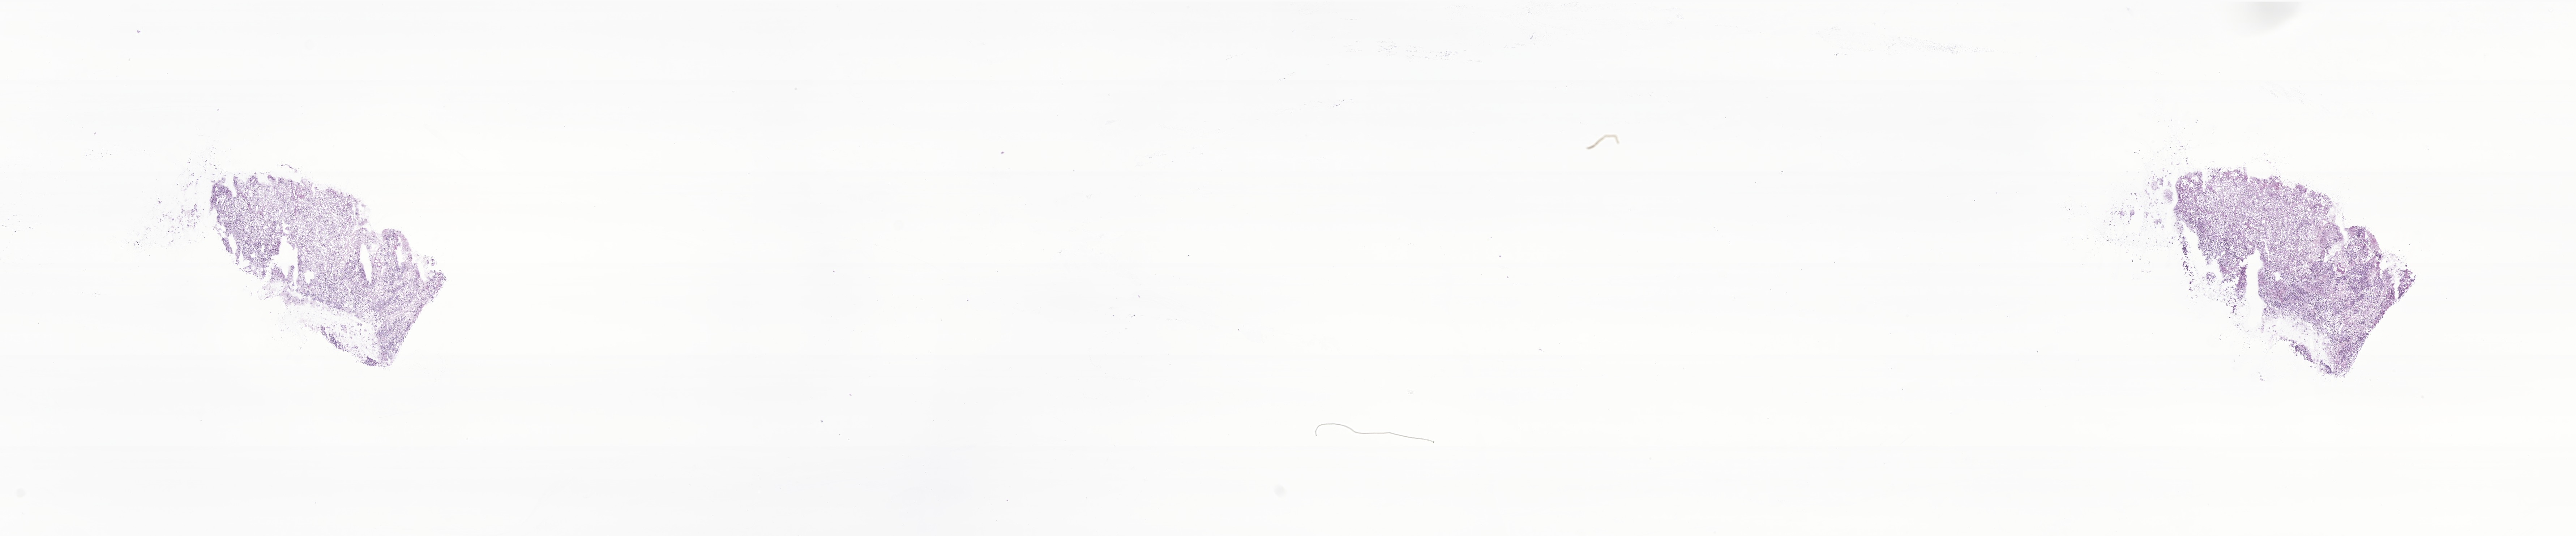
Whole-slide image, H&E stain of tumor tissue from the adrenal gland — whole scanned area (about 30.0 x 6.3 mm) shown as a low-resolution overview, frozen section (OCT-embedded). Male patient, age 78 months (6 years 6 months).
* diagnosis (ICD-O-3 morphology term): Neuroblastoma, NOS